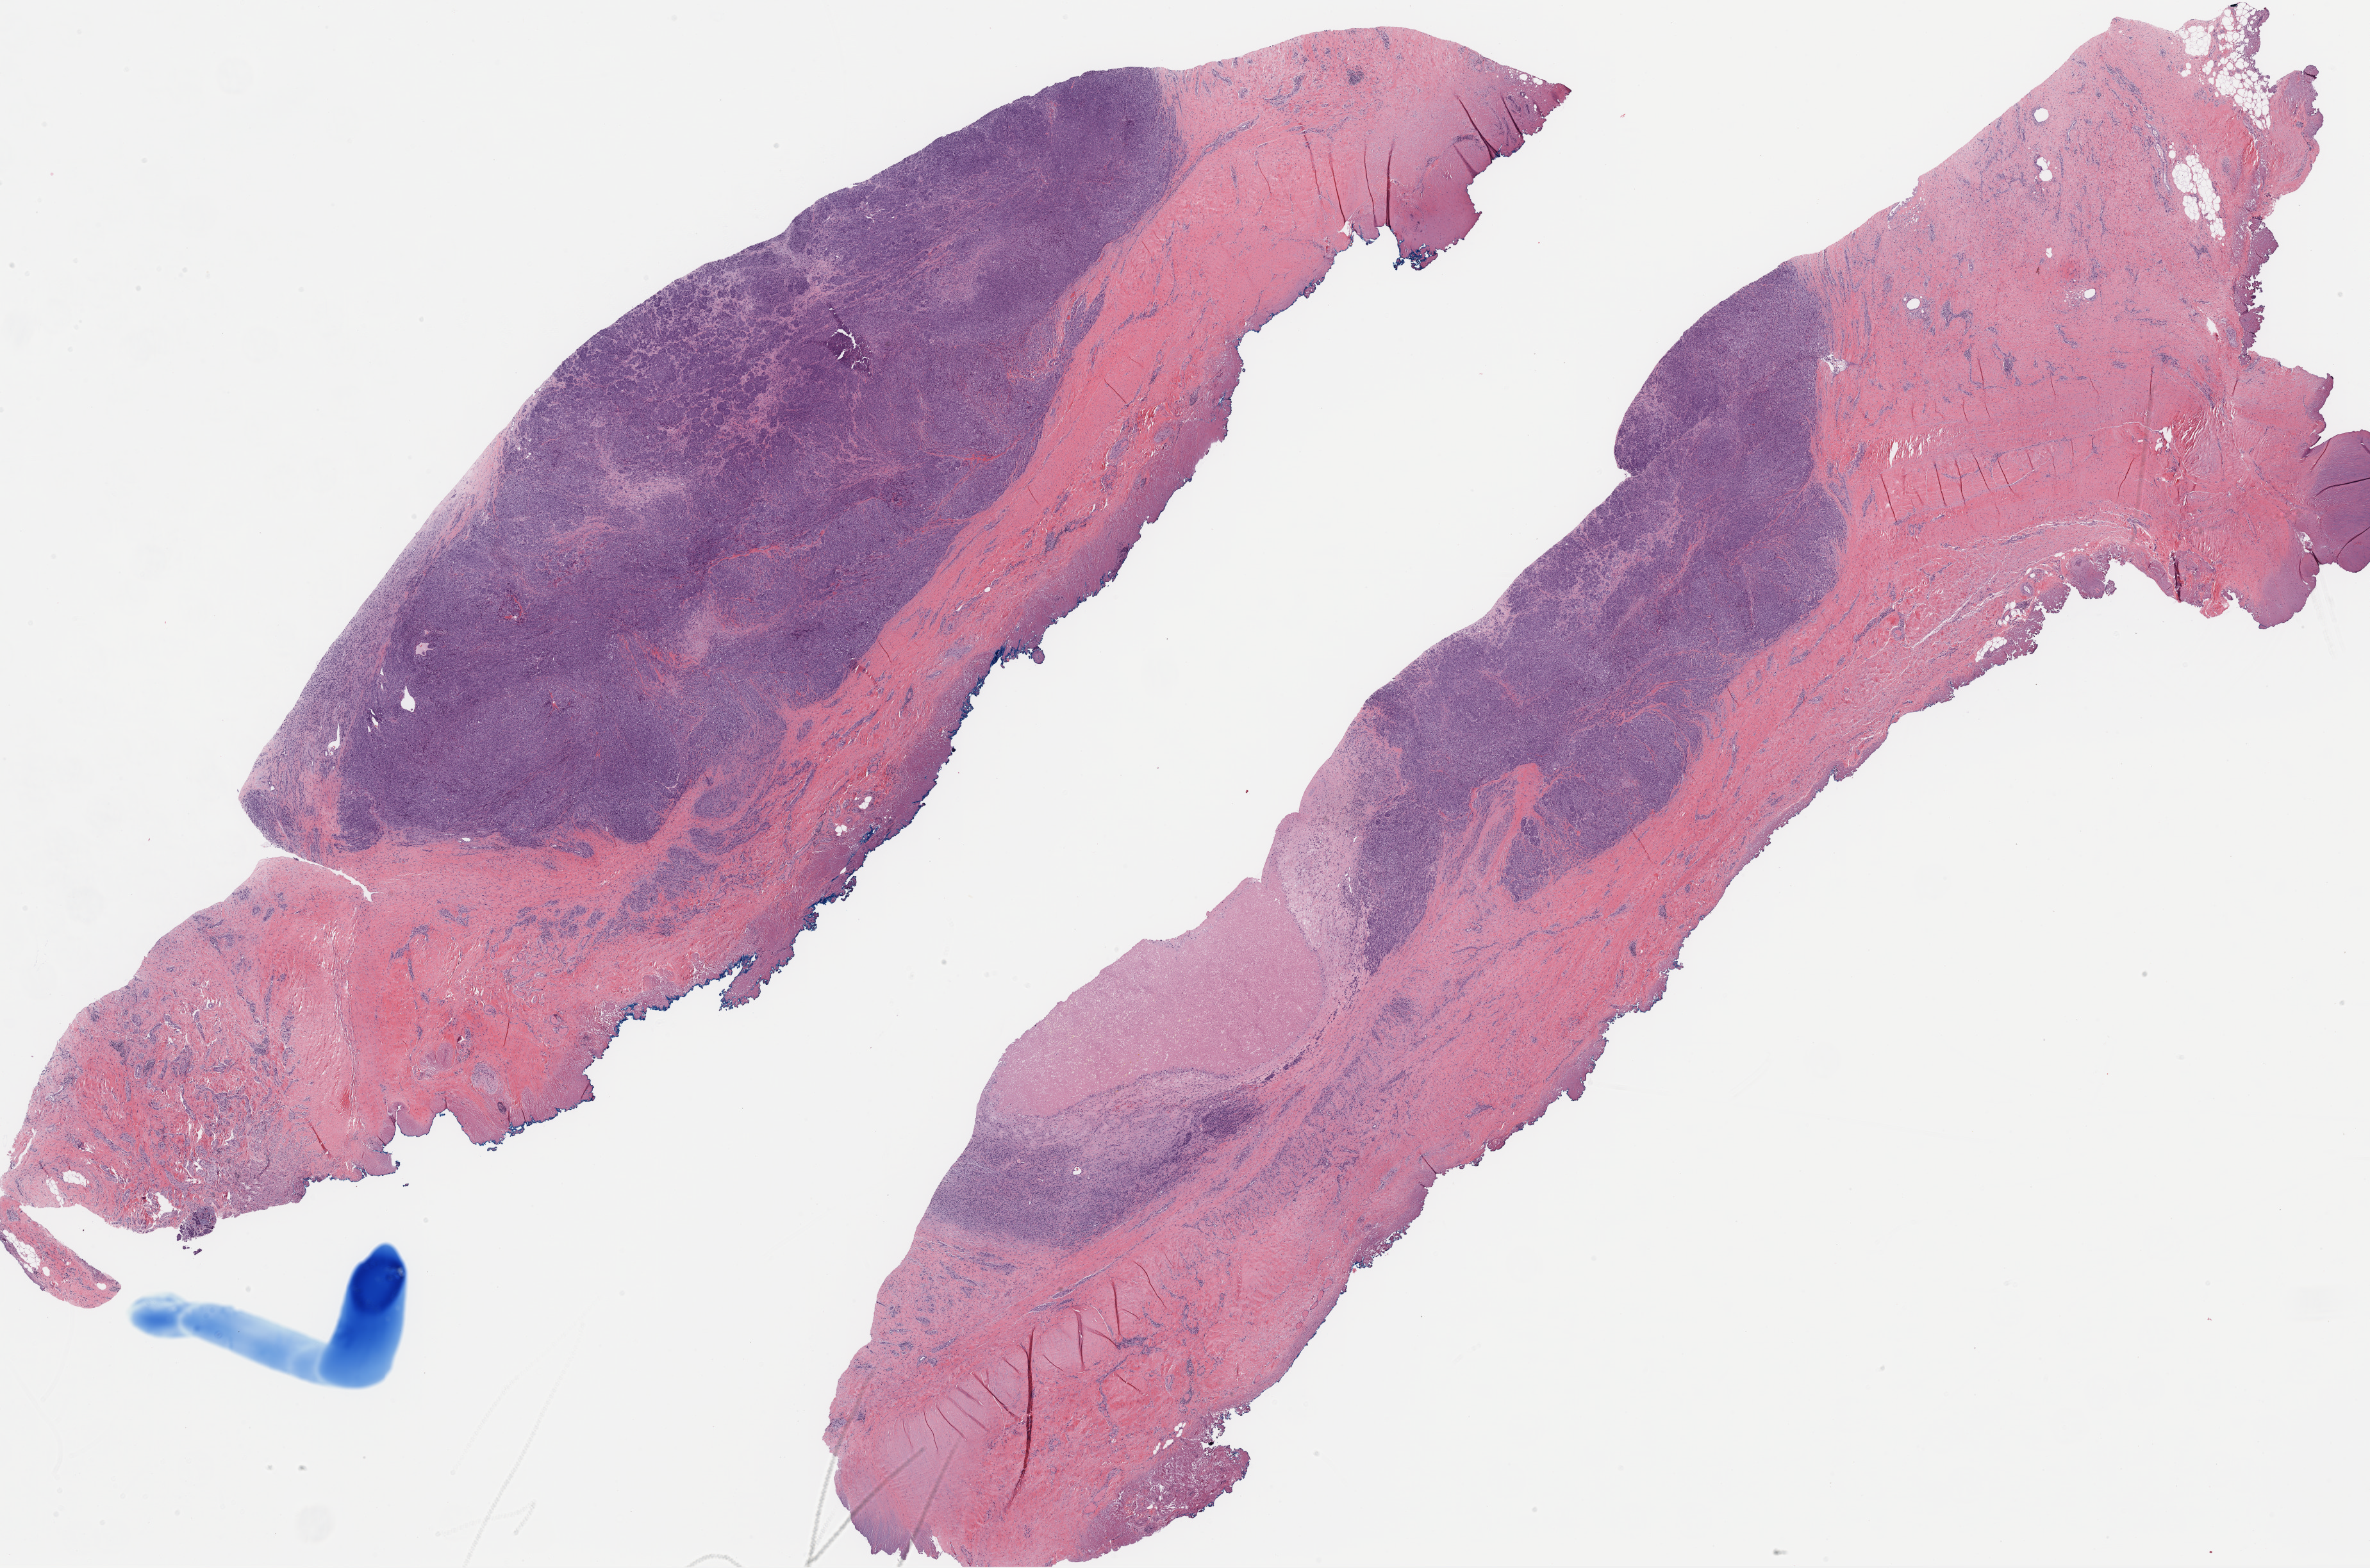
H&E whole-slide image — shown as a low-resolution overview of the whole scanned area (about 29.8 x 19.7 mm, from a 20x scan), formalin-fixed paraffin-embedded (FFPE) diagnostic section, metastatic tumour sample, sampled site not recorded. Female, age 38 years at initial diagnosis.
This section: metastatic tumour tissue. Patient diagnosis: Malignant melanoma, NOS.